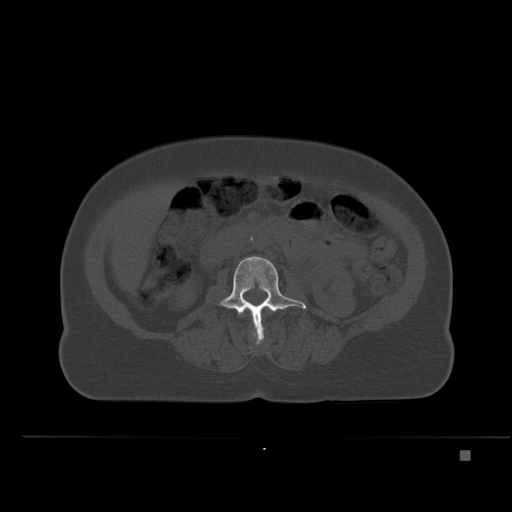
CT including the spine, one axial slice; slice 199 of 477 in the series (ordered by position); bone window (W 1800 / L 400 HU); 1.5 mm slice thickness; 512 × 512 image matrix, field of view 422 × 422 mm. Patient: female, 74 years. Case-level facts recorded for this patient, not image findings: primary cancer: colon.
Structures marked on this image (semi-automatically segmented with operator editing):
- L2 vertebra: bounding box (x1, y1, x2, y2) in pixels: (253, 328, 263, 343)
- L3 vertebra: (218, 256, 306, 343)